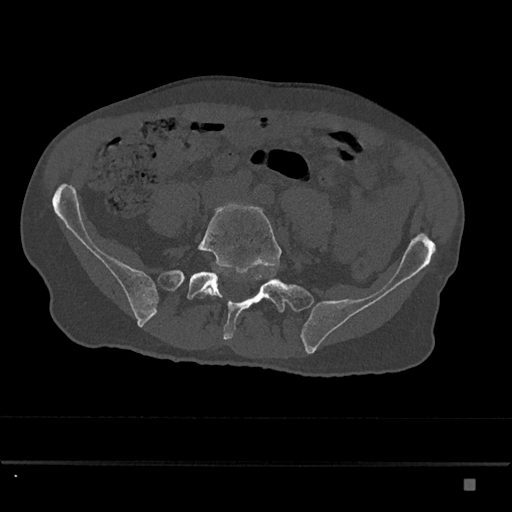
CT including the spine, one axial slice; reconstruction kernel Br40s/3; bone window (W 1800 / L 400 HU); 0.5 mm slice thickness; 512 × 512 image matrix, field of view 390 × 390 mm. Male patient, age 72 years. Case-level facts recorded for this patient, not image findings: primary cancer: prostate.
Structures marked on this image (semi-automatic segmentation, software-assisted and operator-edited):
- L5 vertebra: box from (x=198, y=203) to (x=282, y=298) px